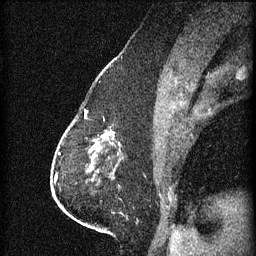
Breast MRI (dynamic contrast-enhanced), one sagittal slice. Slice 28 of 60 in the series (ordered by position). 3 images stored at this slice position (order not interpretable as contrast timing). 1.5 T. TE 4.2 ms, TR 11 ms. 1.5 mm slice thickness. 256 × 256 image matrix, field of view 180 × 180 mm. Female patient, age 63 years.
Outlined on this slice (semi-automatically segmented with operator editing):
- analysis volume of interest (the breast-tissue region the enhancement analysis was run in; not a lesion): bounding box [x1, y1, x2, y2] px = [88, 128, 123, 153]
- tumour enhancement mask (voxels above the 70 % enhancement threshold inside the analysis volume of interest): [90, 132, 115, 151]